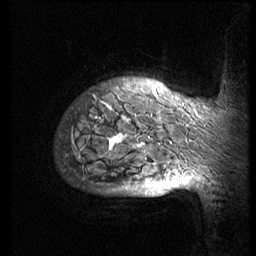
Breast MRI (dynamic contrast-enhanced), one sagittal slice. 3 images stored at this slice position (order not interpretable as contrast timing). 1.5 T. TE 4.2 ms, TR 8.9 ms. 2.5 mm slice thickness. 256 × 256 image matrix, field of view 200 × 200 mm. Female patient, age 57 years. Case-level facts recorded for this patient, not image findings: setting: breast cancer imaged before/during neoadjuvant chemotherapy; receptor status: HER2-positive.
Annotated regions visible in this slice (semi-automatically segmented with operator editing):
- analysis volume of interest (the breast-tissue region the enhancement analysis was run in; not a lesion): box from (x=55, y=68) to (x=247, y=173) px
- tumour enhancement mask (voxels above the 140 % enhancement threshold inside the analysis volume of interest): (x=107, y=89)–(x=195, y=173)